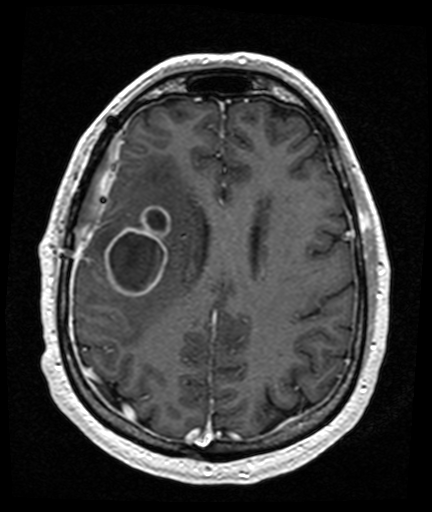
Brain MRI from a brain-tumour surgery series, one axial slice. Slice 57 of 176 in the series (ordered by position). T1-weighted post-contrast. 1 mm slice thickness. 432 × 512 image matrix. From the clinical record (not read from this slice): histopathology: Glioblastoma; WHO grade: 4; IDH mutation: no.
Outlined on this slice (outlined manually by an expert reader):
- tumour: bounding box [x1, y1, x2, y2] px = [105, 207, 171, 297]